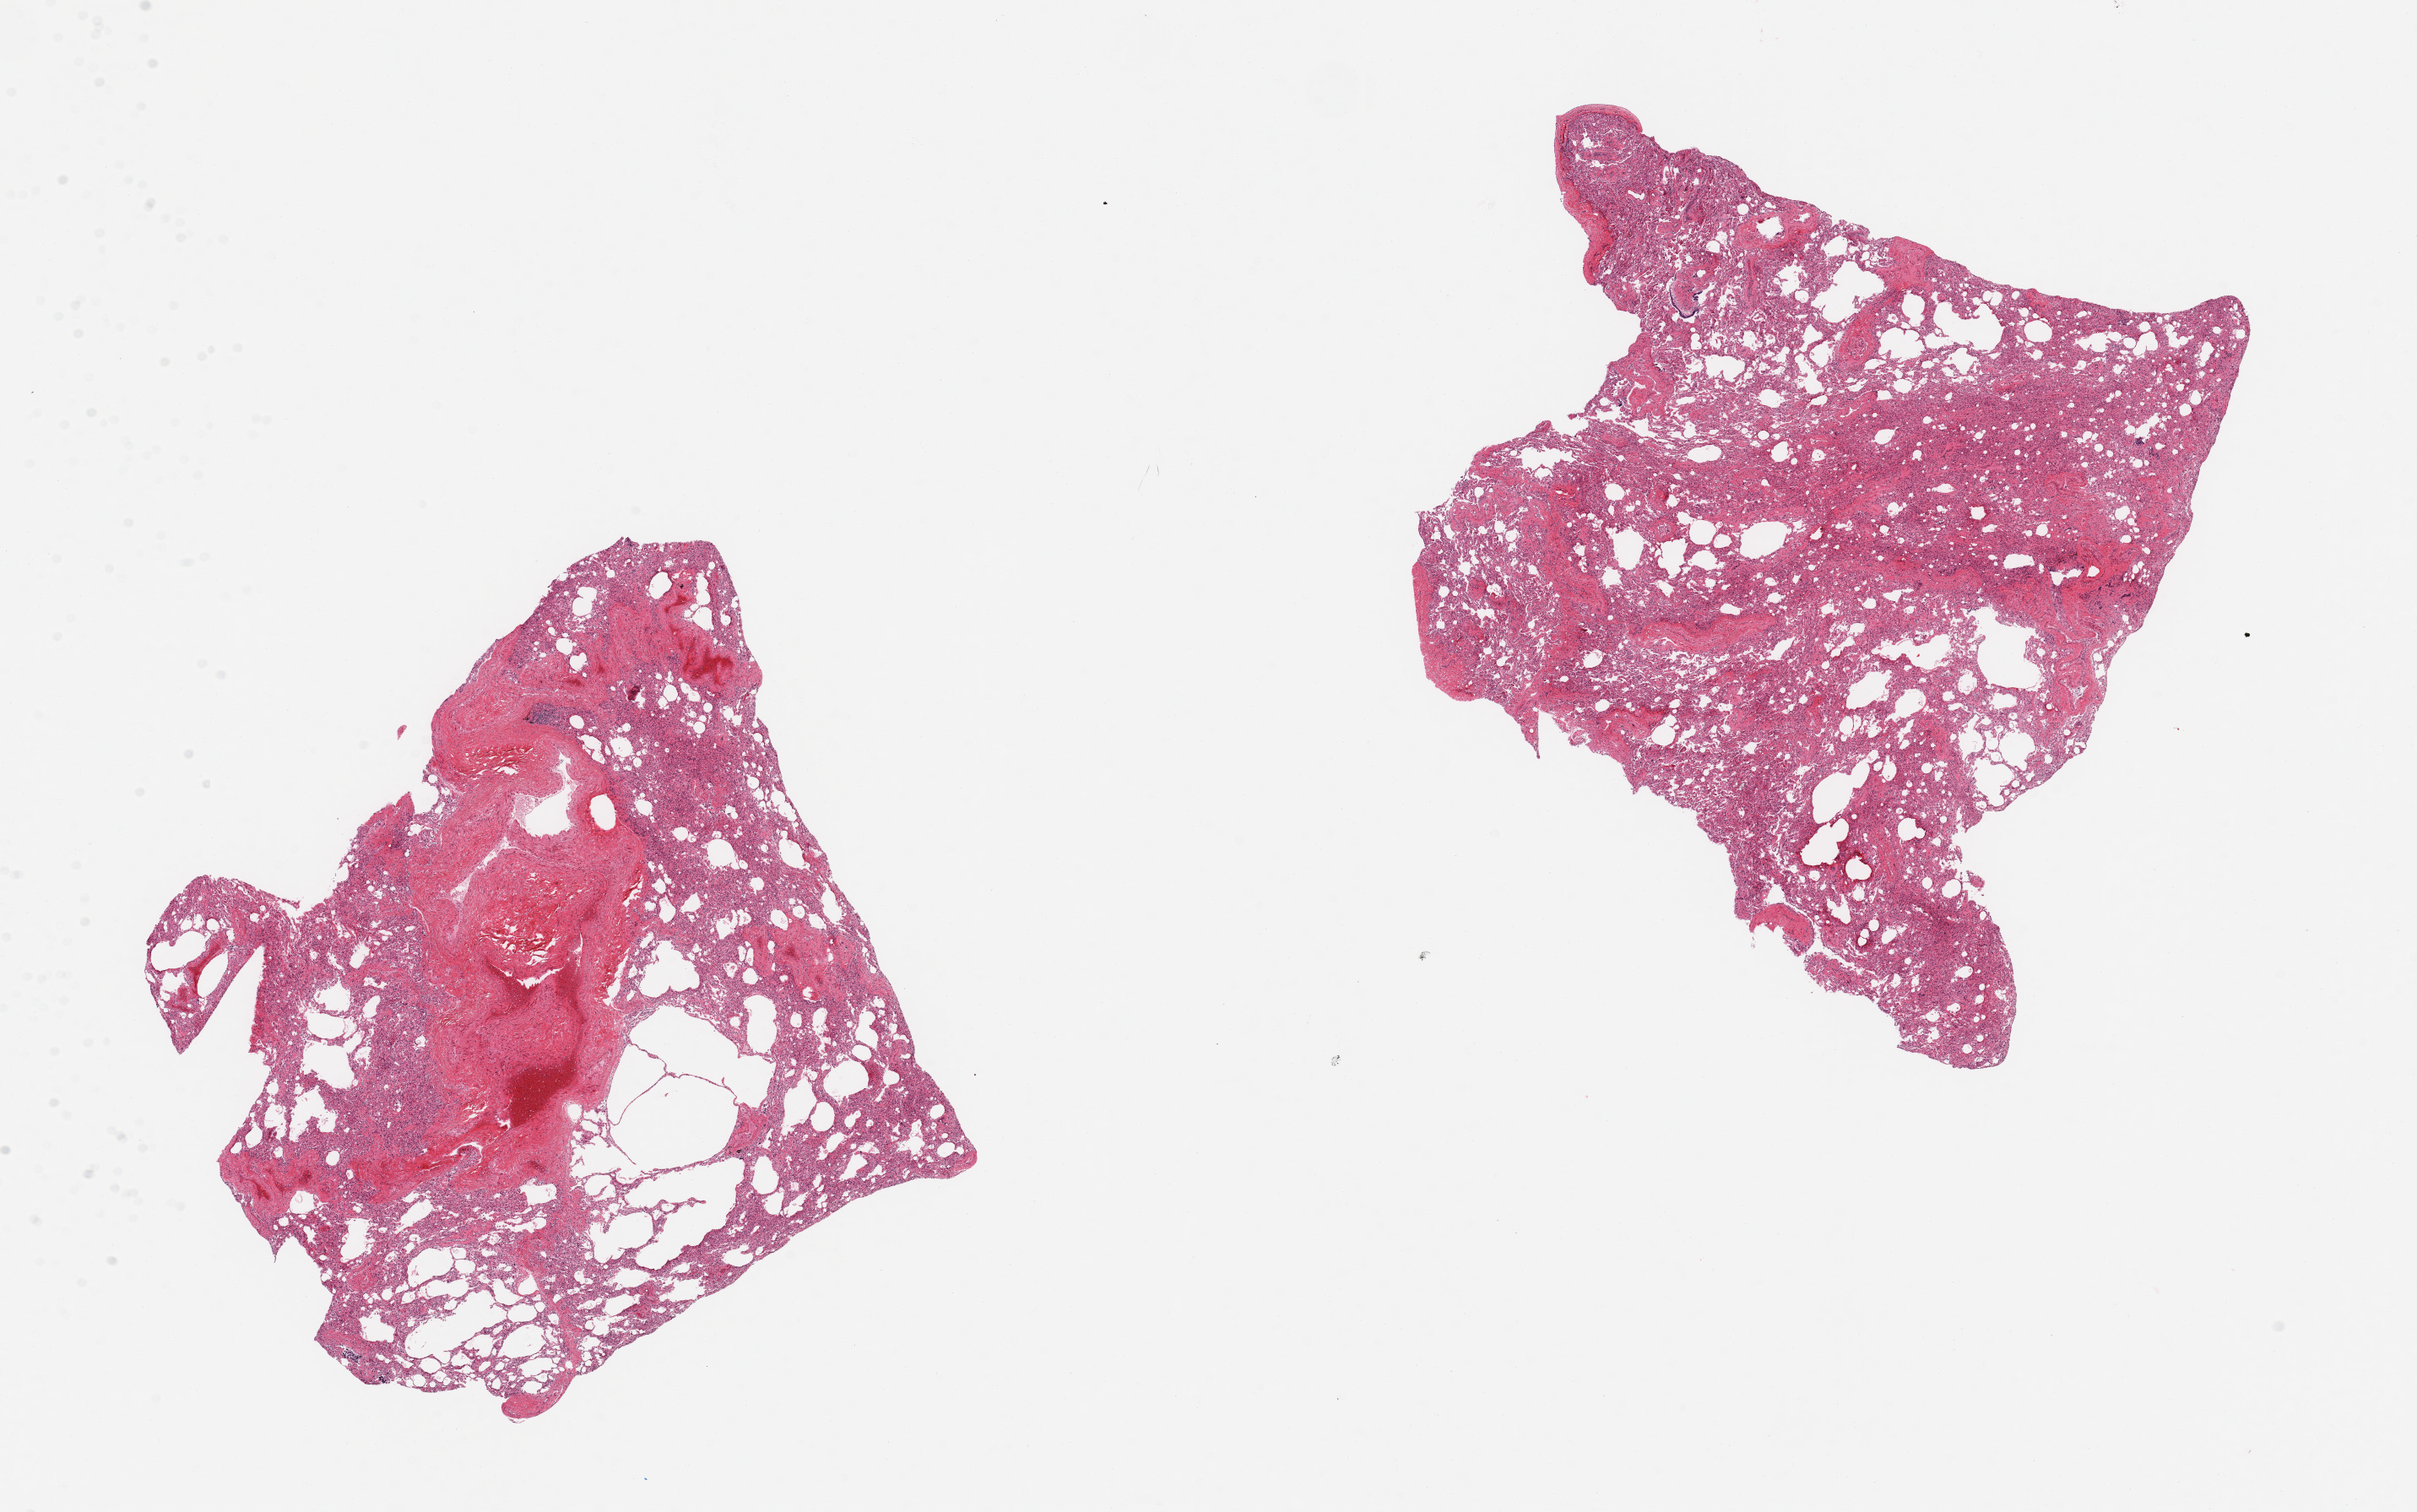
Digitized haematoxylin and eosin-stained section, a low-resolution overview of the entire scanned area, about 22.6 x 14.2 mm (from a 20x scan); PAXgene-fixed, paraffin-embedded tissue; target tissue: lung; tissue donor sample.
Reviewer comment on this tissue sample: 2 pieces, moderate-severe congestion.